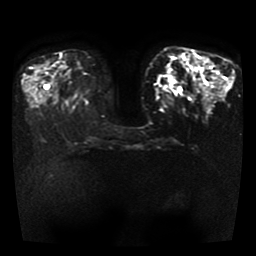
Breast MRI, one axial slice. Slice 13 of 41 in the series (ordered by position). Diffusion-weighted series; image 2 of 4 stored at this slice position (different b-values; order by instance number). 1.5 T. 256 × 256 image matrix. Female patient.
Structures marked on this image (outlined manually by an expert reader):
- tumour on diffusion-weighted imaging: bounding box [x1, y1, x2, y2] px = [162, 79, 176, 91]